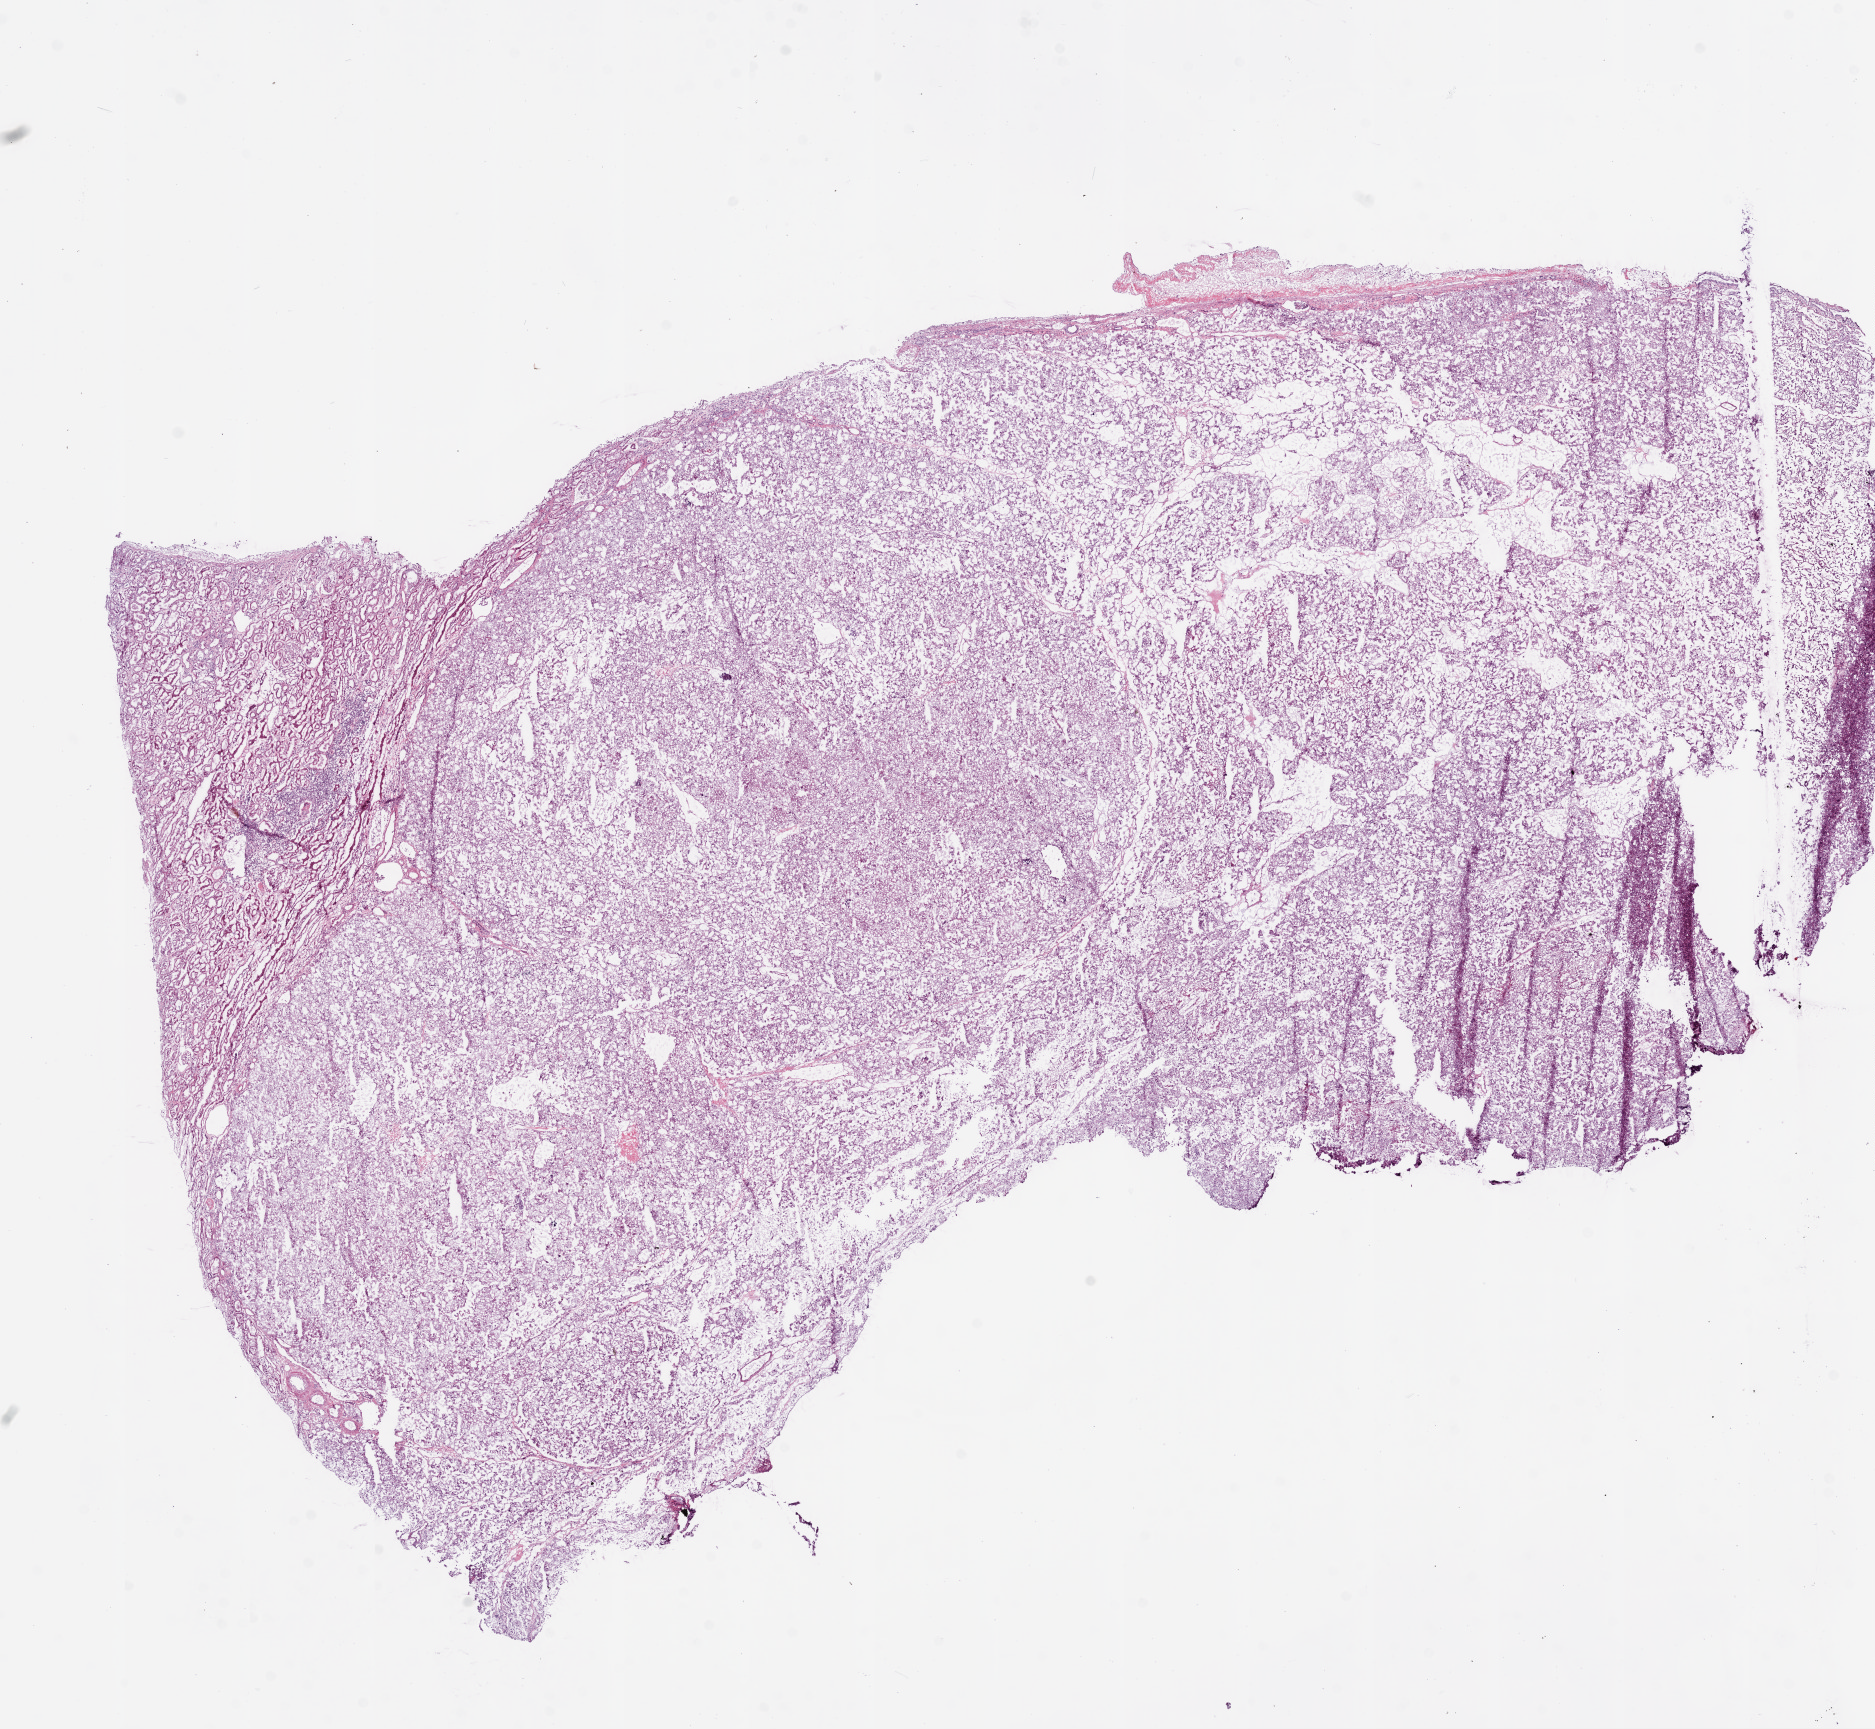
Hematoxylin and eosin (H&E) stained whole-slide image — low-resolution overview of the scanned area, about 15.0 x 13.9 mm, frozen section from the bottom of the tissue portion, kidney, primary tumour sample. Patient: male, age at initial diagnosis 54 years. Composition of this section per pathologist review: tumour cells 75%, tumour nuclei 80%.
Histologic diagnosis: Clear cell adenocarcinoma, NOS.